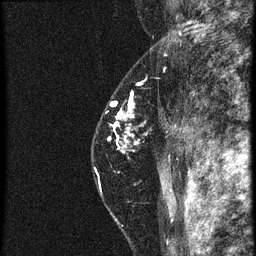
Breast MRI (dynamic contrast-enhanced), one sagittal slice; position 46 of 60 along the scan axis; 4 images stored at this slice position (order not interpretable as contrast timing); 1.5 T; TE 4.2 ms, TR 20.4 ms; 256 × 256 image matrix. Female patient, age 46 years. Case-level facts recorded for this patient, not image findings: setting: breast cancer imaged before/during neoadjuvant chemotherapy; receptor status: triple-negative.
Outlined on this slice (semi-automatic segmentation, software-assisted and operator-edited):
- analysis volume of interest (the breast-tissue region the enhancement analysis was run in; not a lesion): bounding box <90,82,181,185> (left, top, right, bottom; pixels)
- tumour enhancement mask (voxels above the 90 % enhancement threshold inside the analysis volume of interest): <98,102,133,179>